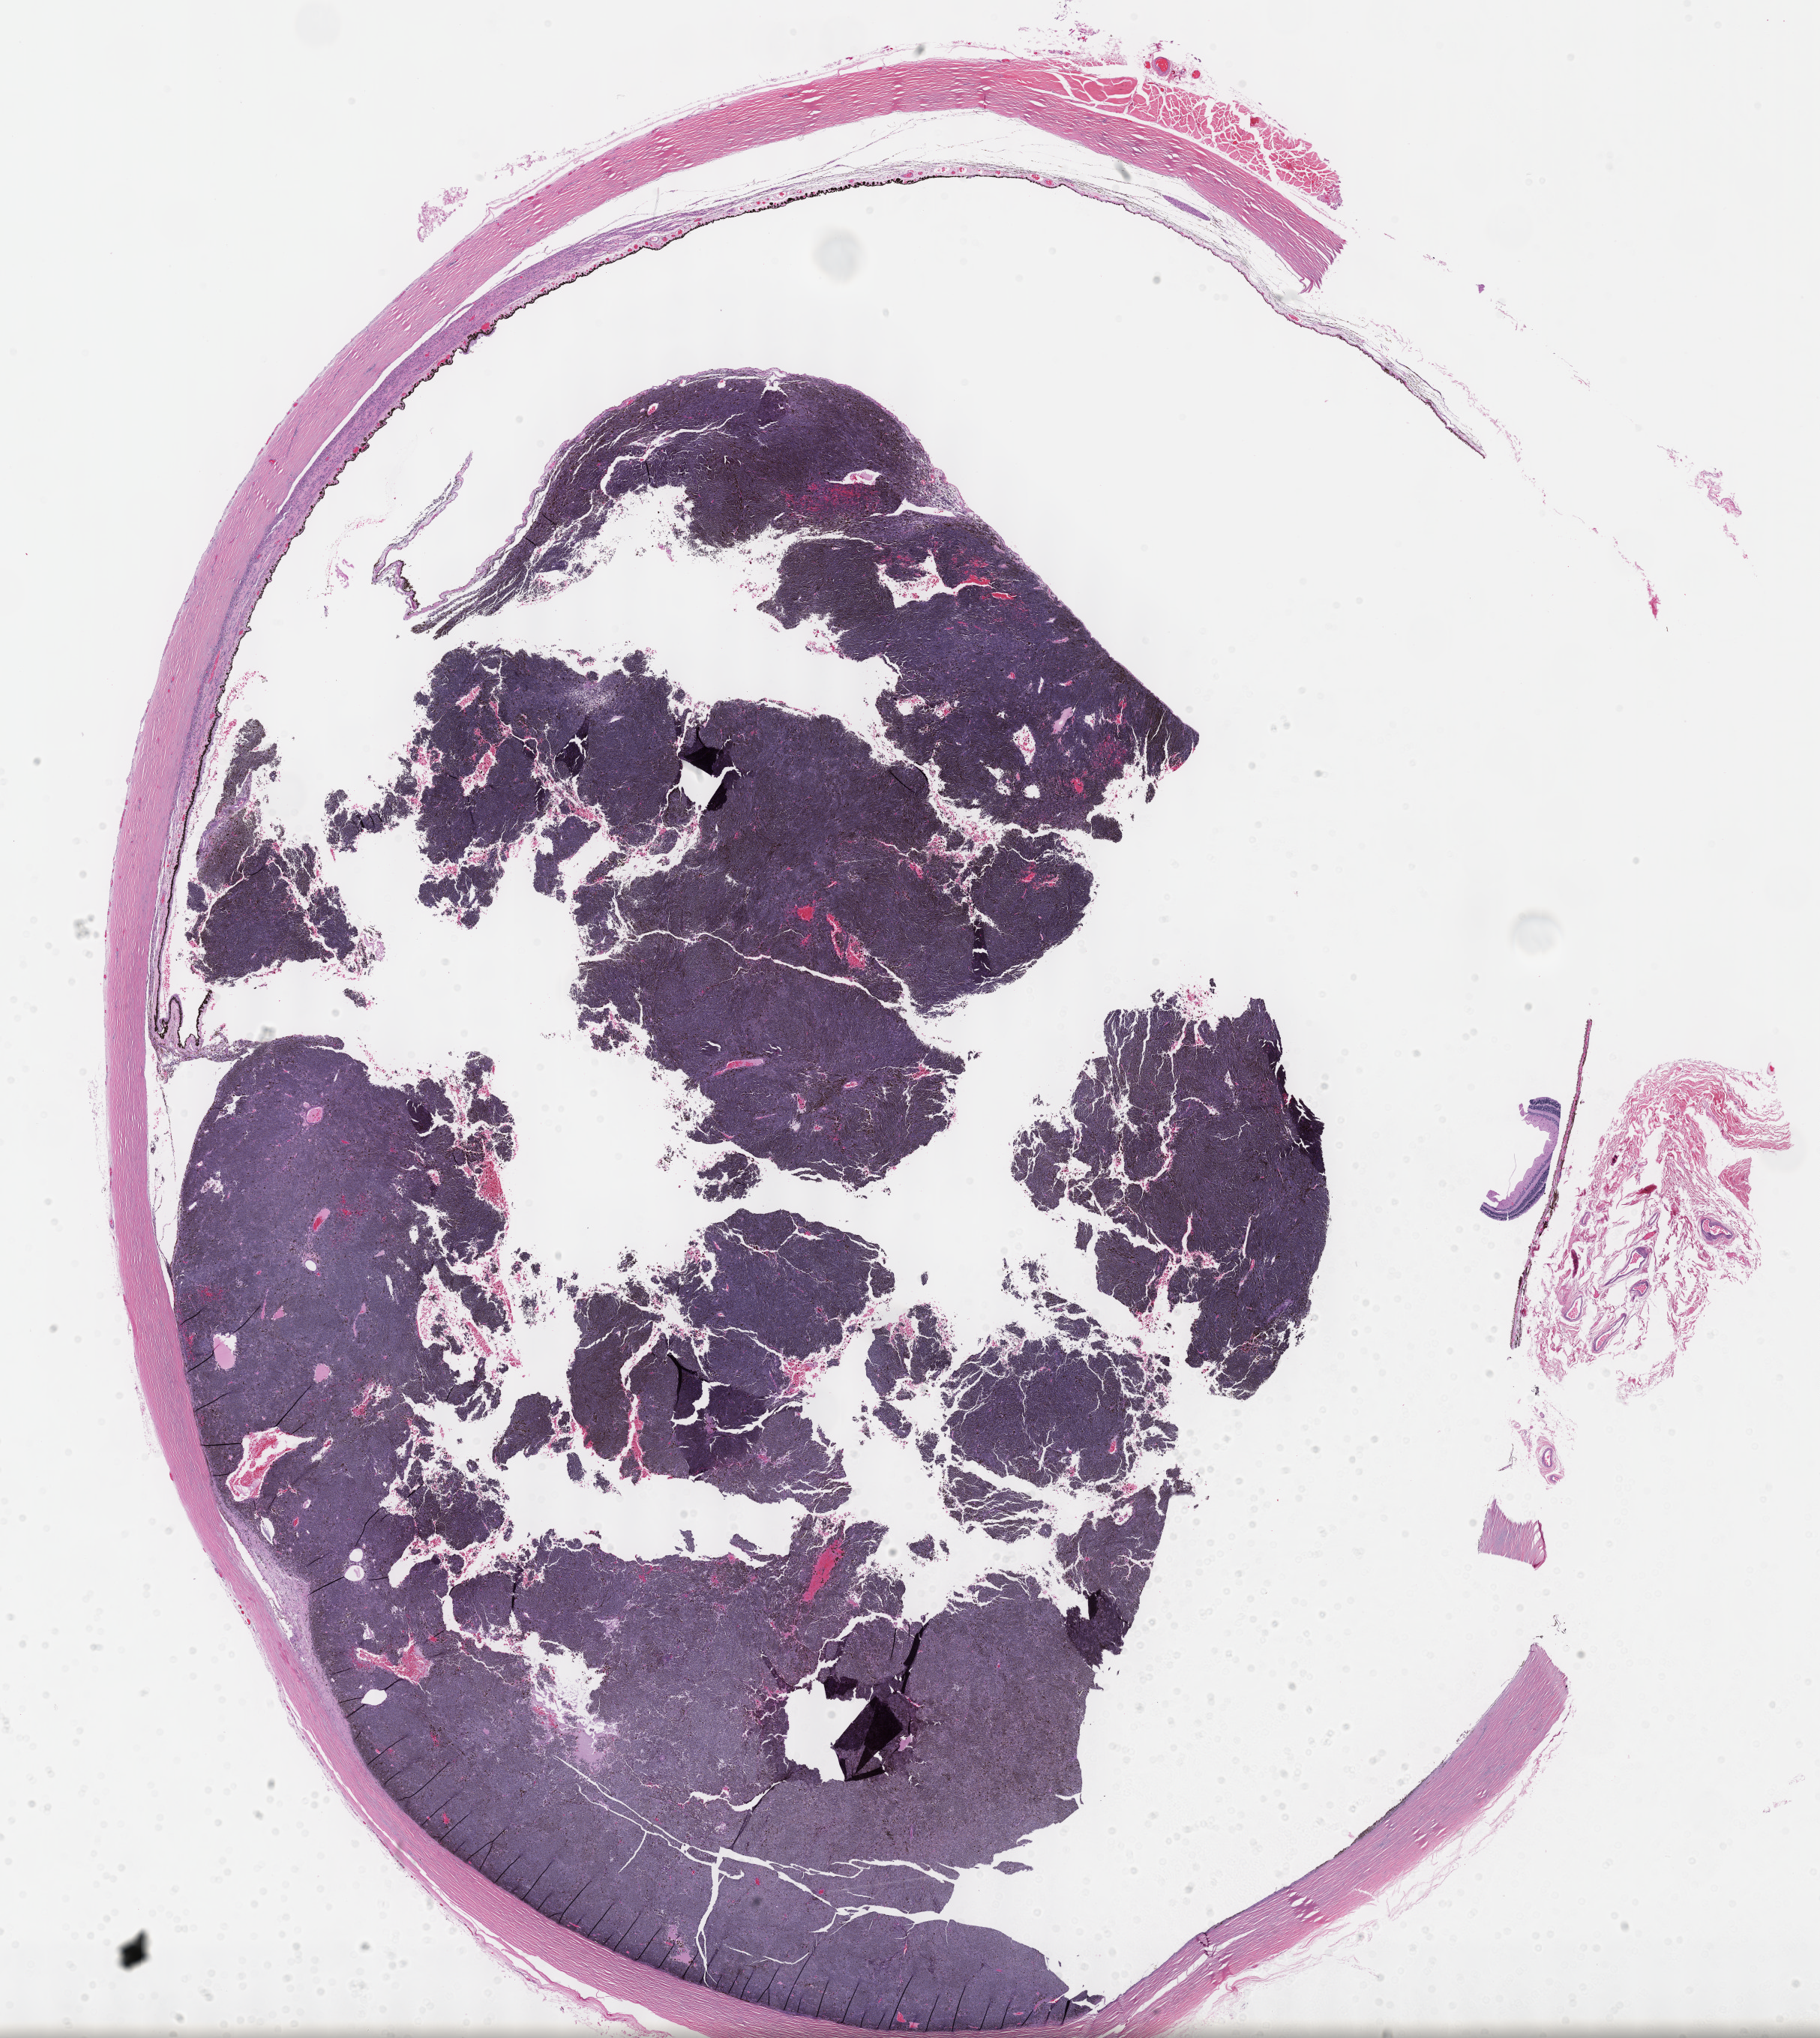
Digitized Hematoxylin and eosin (H&E) stained tissue section (whole slide), low-resolution overview of the scanned area, about 19.6 x 22.0 mm (acquisition: 40x scan), formalin-fixed paraffin-embedded (FFPE) diagnostic section, sample: primary tumour, uvea. Patient: male, age at initial diagnosis 75 years.
AJCC pathologic stage: IIB (7th edition). Diagnosis: Spindle cell melanoma, NOS (choroid).